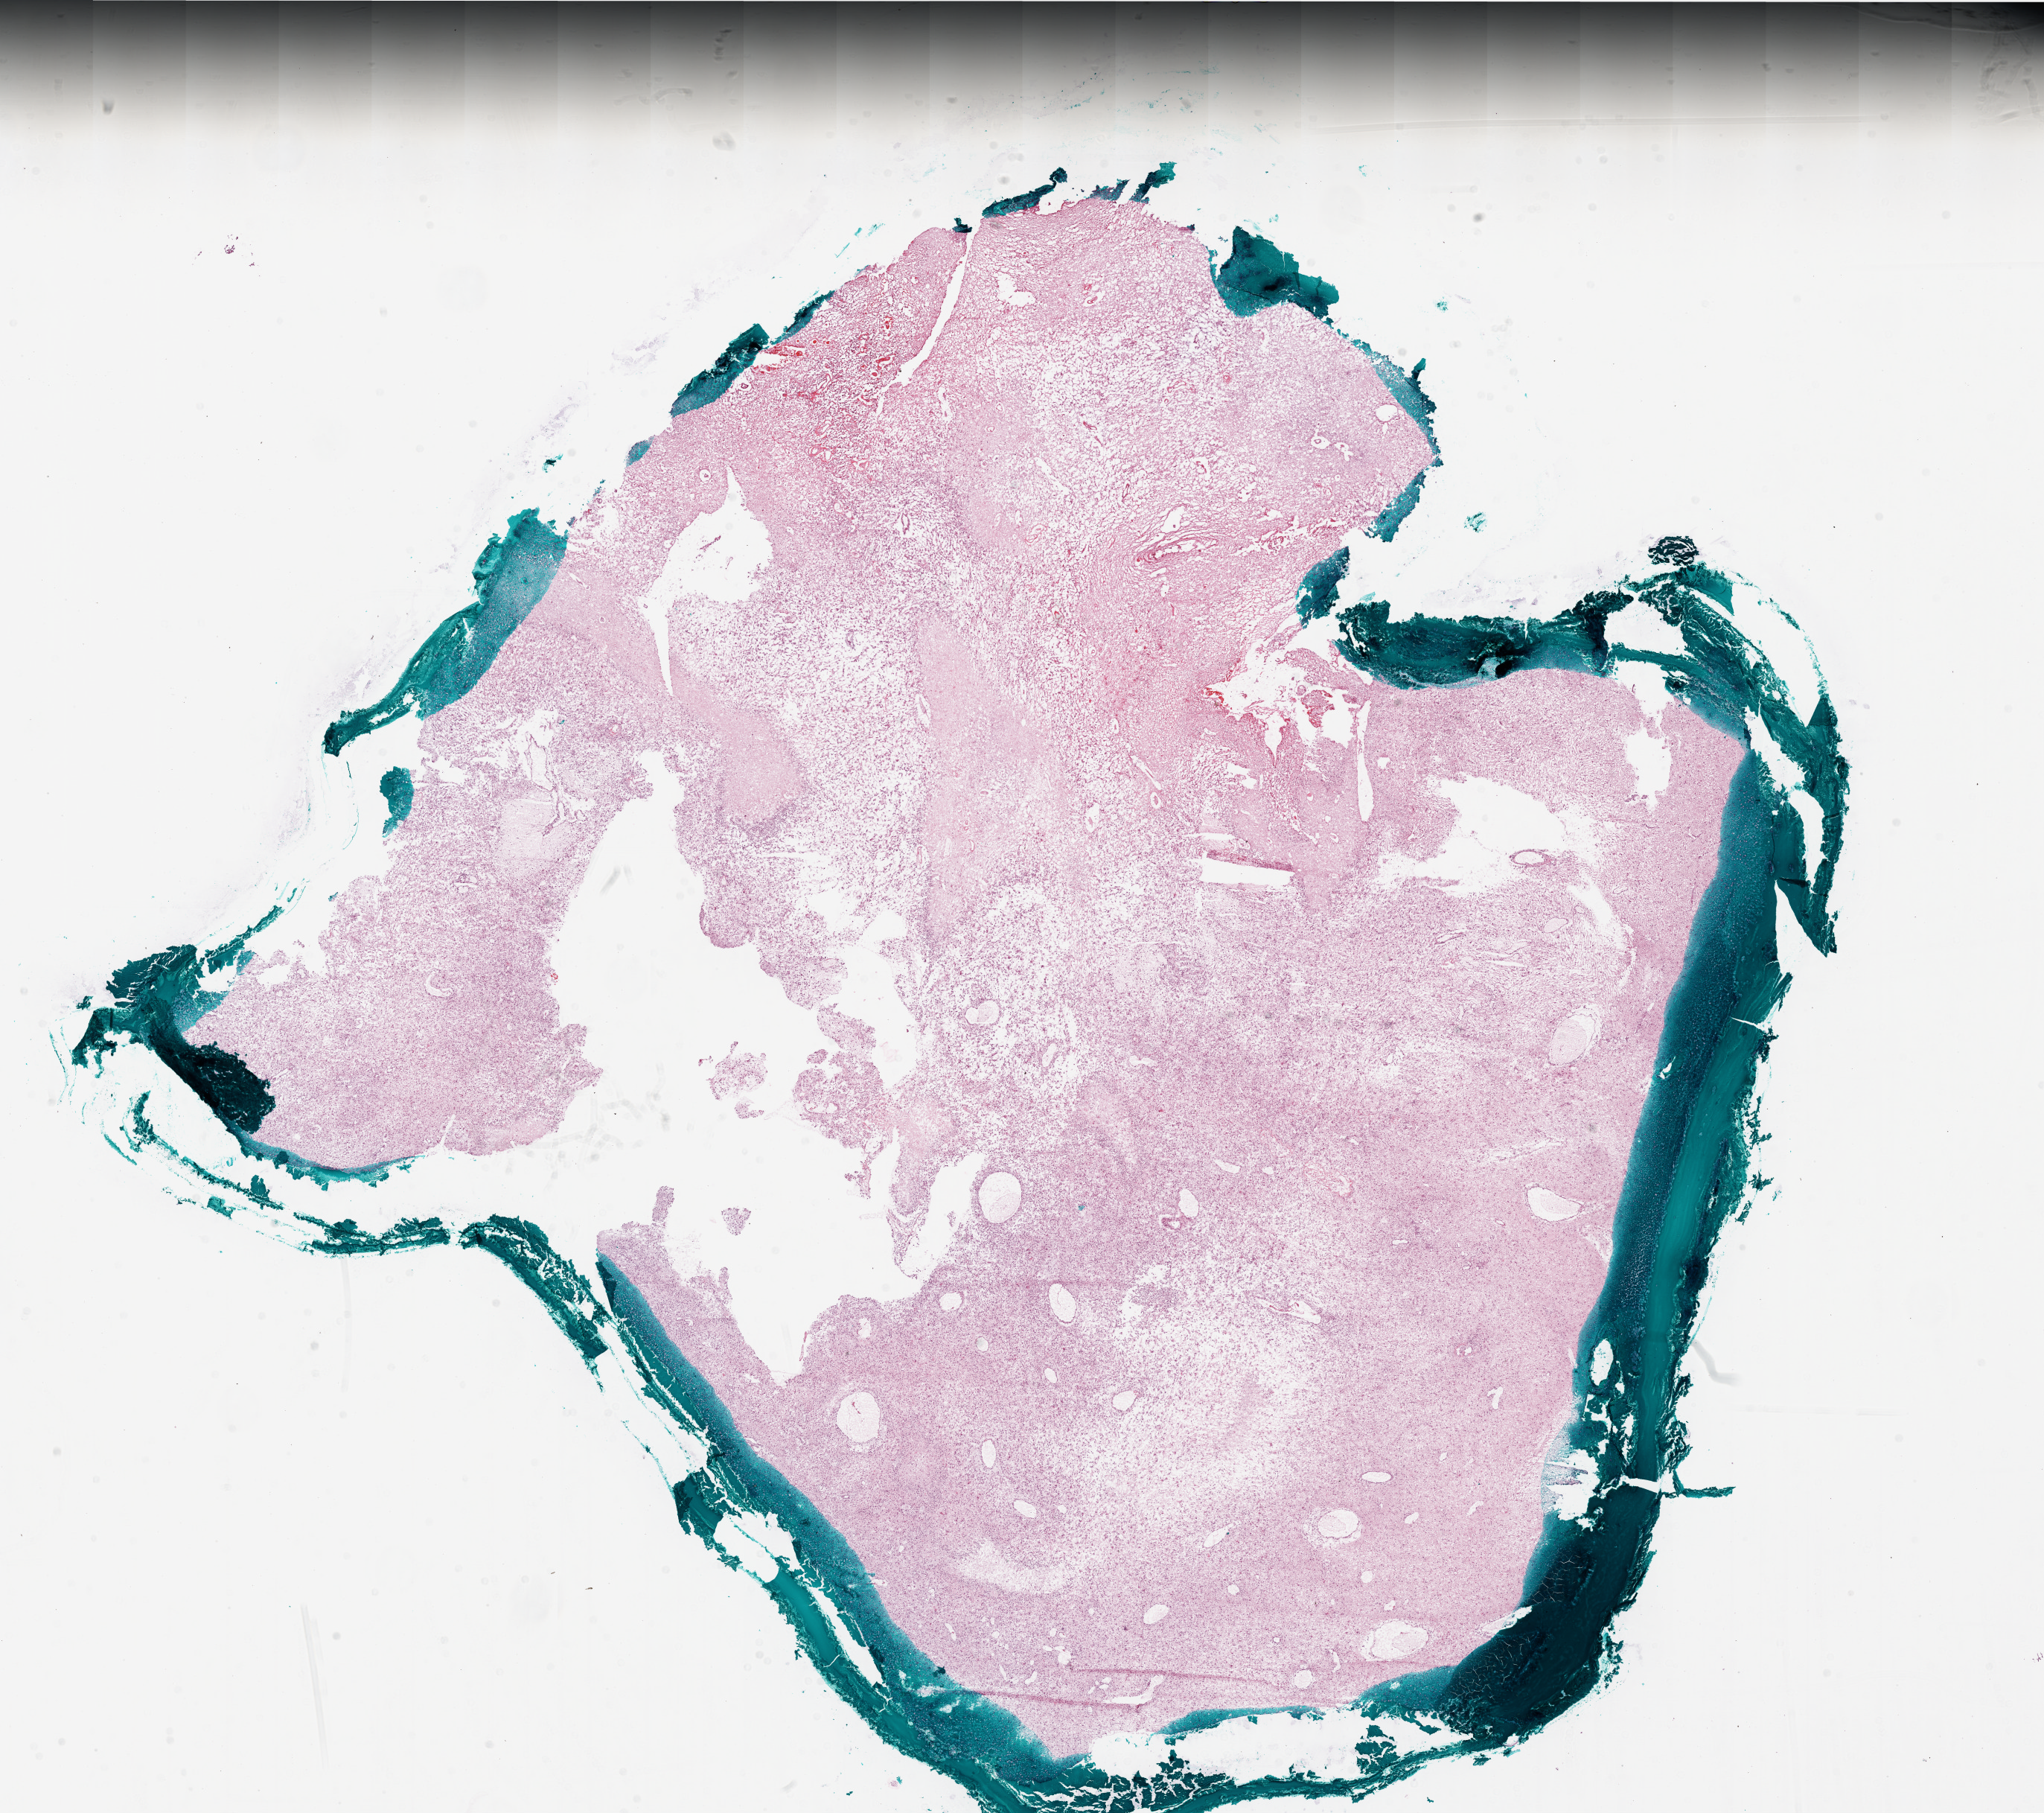
Hematoxylin and eosin (H&E) stained whole-slide image — a low-resolution overview of the entire scanned area, about 22.0 x 19.5 mm (from a 20x scan); frozen section; primary tumour sample from the brain. Patient: male, age at initial diagnosis 56 years. Slide review estimates, as recorded: tumour cells 50%, tumour nuclei 90%, normal cells 0%, stromal cells 25%, necrosis 25%.
Diagnosis: Glioblastoma.